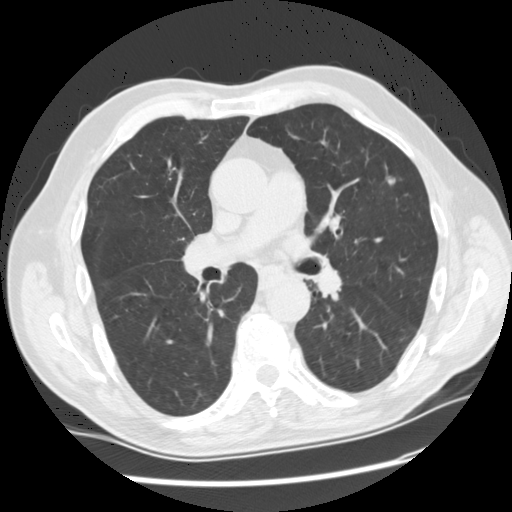
Axial slice from a low-dose chest CT screening exam, third screening round (two years after baseline), lung window (W 1500 / L -600 HU), standard (soft-tissue) reconstruction kernel (STANDARD). Male participant, aged 71 years at enrolment. Current smoker at enrolment.
Lesion marked by an expert reader, bounding box [x1, y1, x2, y2] px = [362, 161, 414, 203]. The screening reader recorded 2 non-calcified nodules or masses ≥4 mm on this exam; which of them this box marks is not recorded. Official screen result: positive, other.